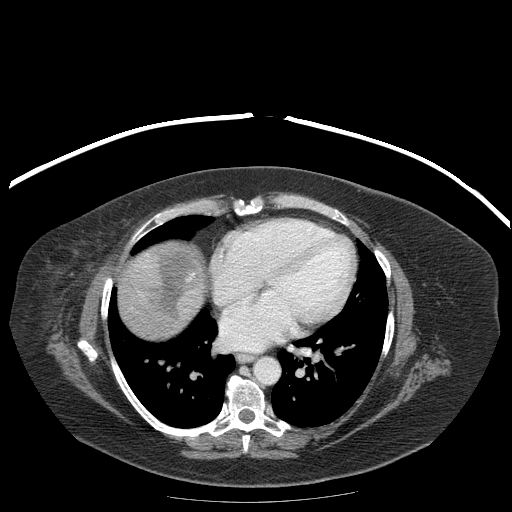
Contrast-enhanced abdominal CT (liver protocol), one axial slice; position 181 of 204 along the scan axis; reconstruction kernel STANDARD; soft-tissue window (W 400 / L 40 HU); 2.5 mm slice thickness; 512 × 512 image matrix, field of view 440 × 440 mm. From the clinical record (not read from this slice): diagnosis: hepatocellular carcinoma (patient treated with transarterial chemoembolisation; whether this scan precedes or follows treatment is not stated here); TNM stage (as recorded): Stage-IIIB; Child-Pugh class: A.
Outlined on this slice (semi-automatically segmented with operator editing):
- liver parenchyma outside the tumour (the mass and vessels are separate outlines, so this box may not span the whole liver): bounding box (x1, y1, x2, y2) in pixels: (118, 242, 184, 338)
- mass: (133, 244, 205, 326)